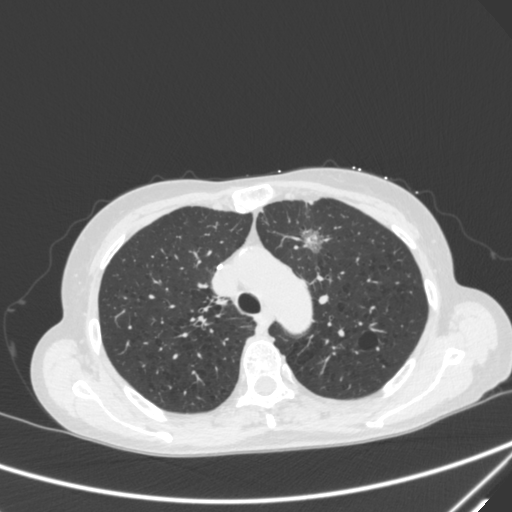
Chest CT, one axial slice. Slice 221 of 300 in the series (ordered by position). 120 kVp. Lung window (W 1500 / L -600 HU). 1 mm slice thickness. 512 × 512 image matrix, field of view 350 × 350 mm. Patient: female, 71 years. From the clinical record (not read from this slice): clinical TNM (as recorded): T1c N0 M0; histopathological grade: G2-3.
Structures marked on this image (rectangle marked by the reading radiologist):
- lung tumour (recorded histology: adenocarcinoma): box from (x=298, y=224) to (x=331, y=261) px